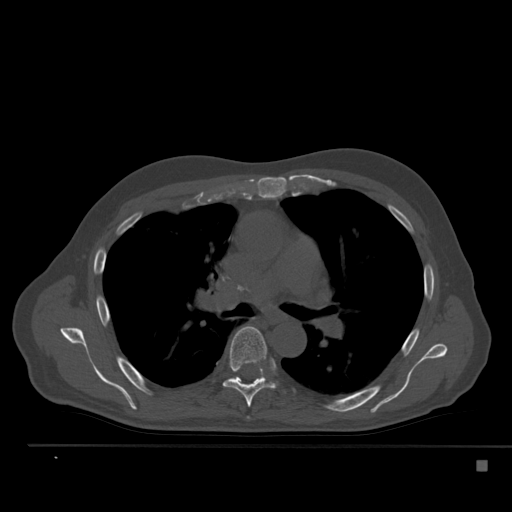
CT including the spine, one axial slice; slice 347 of 517 in the series (ordered by position); 120 kVp; bone window (W 1800 / L 400 HU); 1.5 mm slice thickness; 512 × 512 image matrix, field of view 408 × 408 mm. Patient: male, 70 years. From the clinical record (not read from this slice): primary cancer: renal; vertebrae with lytic lesions (as recorded): T4, T6, T10, T12, L3, L4, L5.
Annotated regions visible in this slice (semi-automatic segmentation, software-assisted and operator-edited):
- T6 vertebra: bounding box [x1, y1, x2, y2] px = [223, 326, 276, 407]
- T7 vertebra: [259, 377, 263, 379]